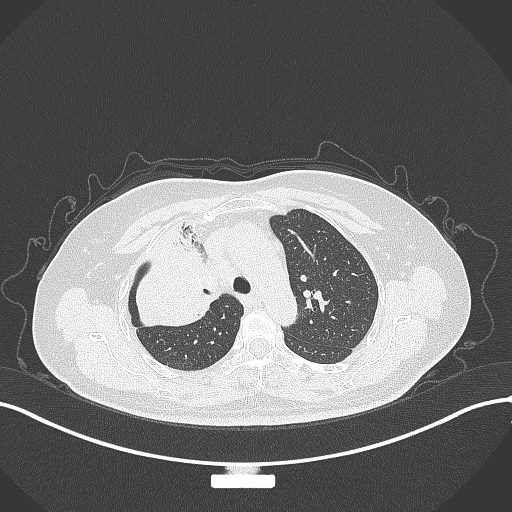
Chest CT, one axial slice; slice 223 of 309 in the series (ordered by position); 120 kVp; lung window (W 1500 / L -600 HU); 1 mm slice thickness; 512 × 512 image matrix, field of view 400 × 400 mm. Patient: female, 60 years. Case-level facts recorded for this patient, not image findings: clinical TNM (as recorded): T3 N1 M1.
Outlined on this slice (bounding box drawn by a radiologist):
- lung tumour (recorded histology: adenocarcinoma): bounding box (x1, y1, x2, y2) in pixels: (122, 220, 224, 333)